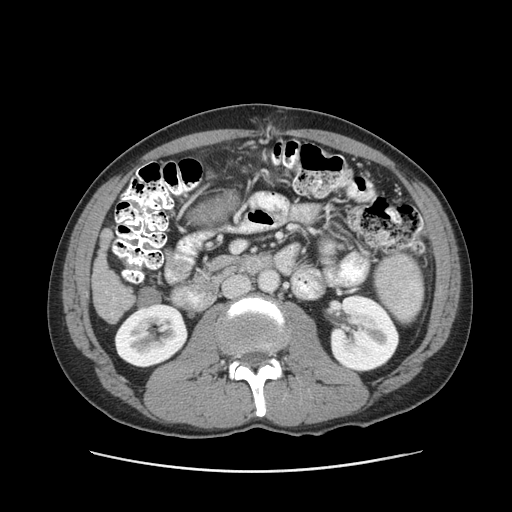
Contrast-enhanced abdominal CT (liver protocol), one axial slice. Slice 29 of 93 in the series (ordered by position). Reconstruction kernel STANDARD. Soft-tissue window (W 400 / L 40 HU). 512 × 512 image matrix, field of view 380 × 380 mm. From the clinical record (not read from this slice): diagnosis: hepatocellular carcinoma (patient treated with transarterial chemoembolisation; whether this scan precedes or follows treatment is not stated here); TNM stage (as recorded): Stage-II; Child-Pugh class: A; tumour size: 1 cm.
Annotated regions visible in this slice (semi-automatic segmentation, software-assisted and operator-edited):
- liver parenchyma outside the tumour (the mass and vessels are separate outlines, so this box may not span the whole liver): bounding box <92,230,134,322> (left, top, right, bottom; pixels)